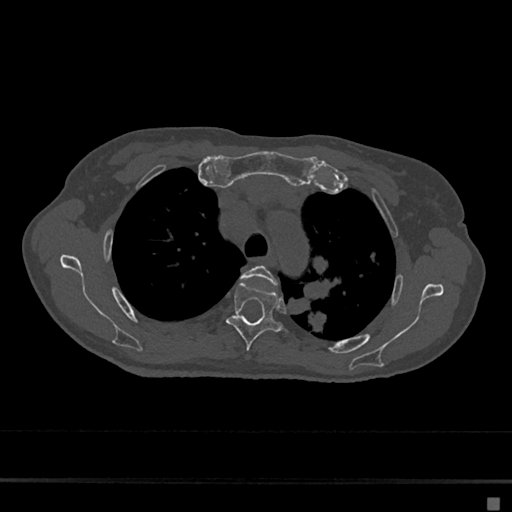
CT including the spine, one axial slice; position 504 of 797 along the scan axis; reconstruction kernel Br40s/3; bone window (W 1800 / L 400 HU); 0.5 mm slice thickness; 512 × 512 image matrix. Patient: female, 68 years. From the clinical record (not read from this slice): primary cancer: renal.
Outlined on this slice (semi-automatic segmentation, software-assisted and operator-edited):
- T3 vertebra: bounding box (x1, y1, x2, y2) in pixels: (241, 265, 277, 285)
- T4 vertebra: (226, 281, 283, 351)